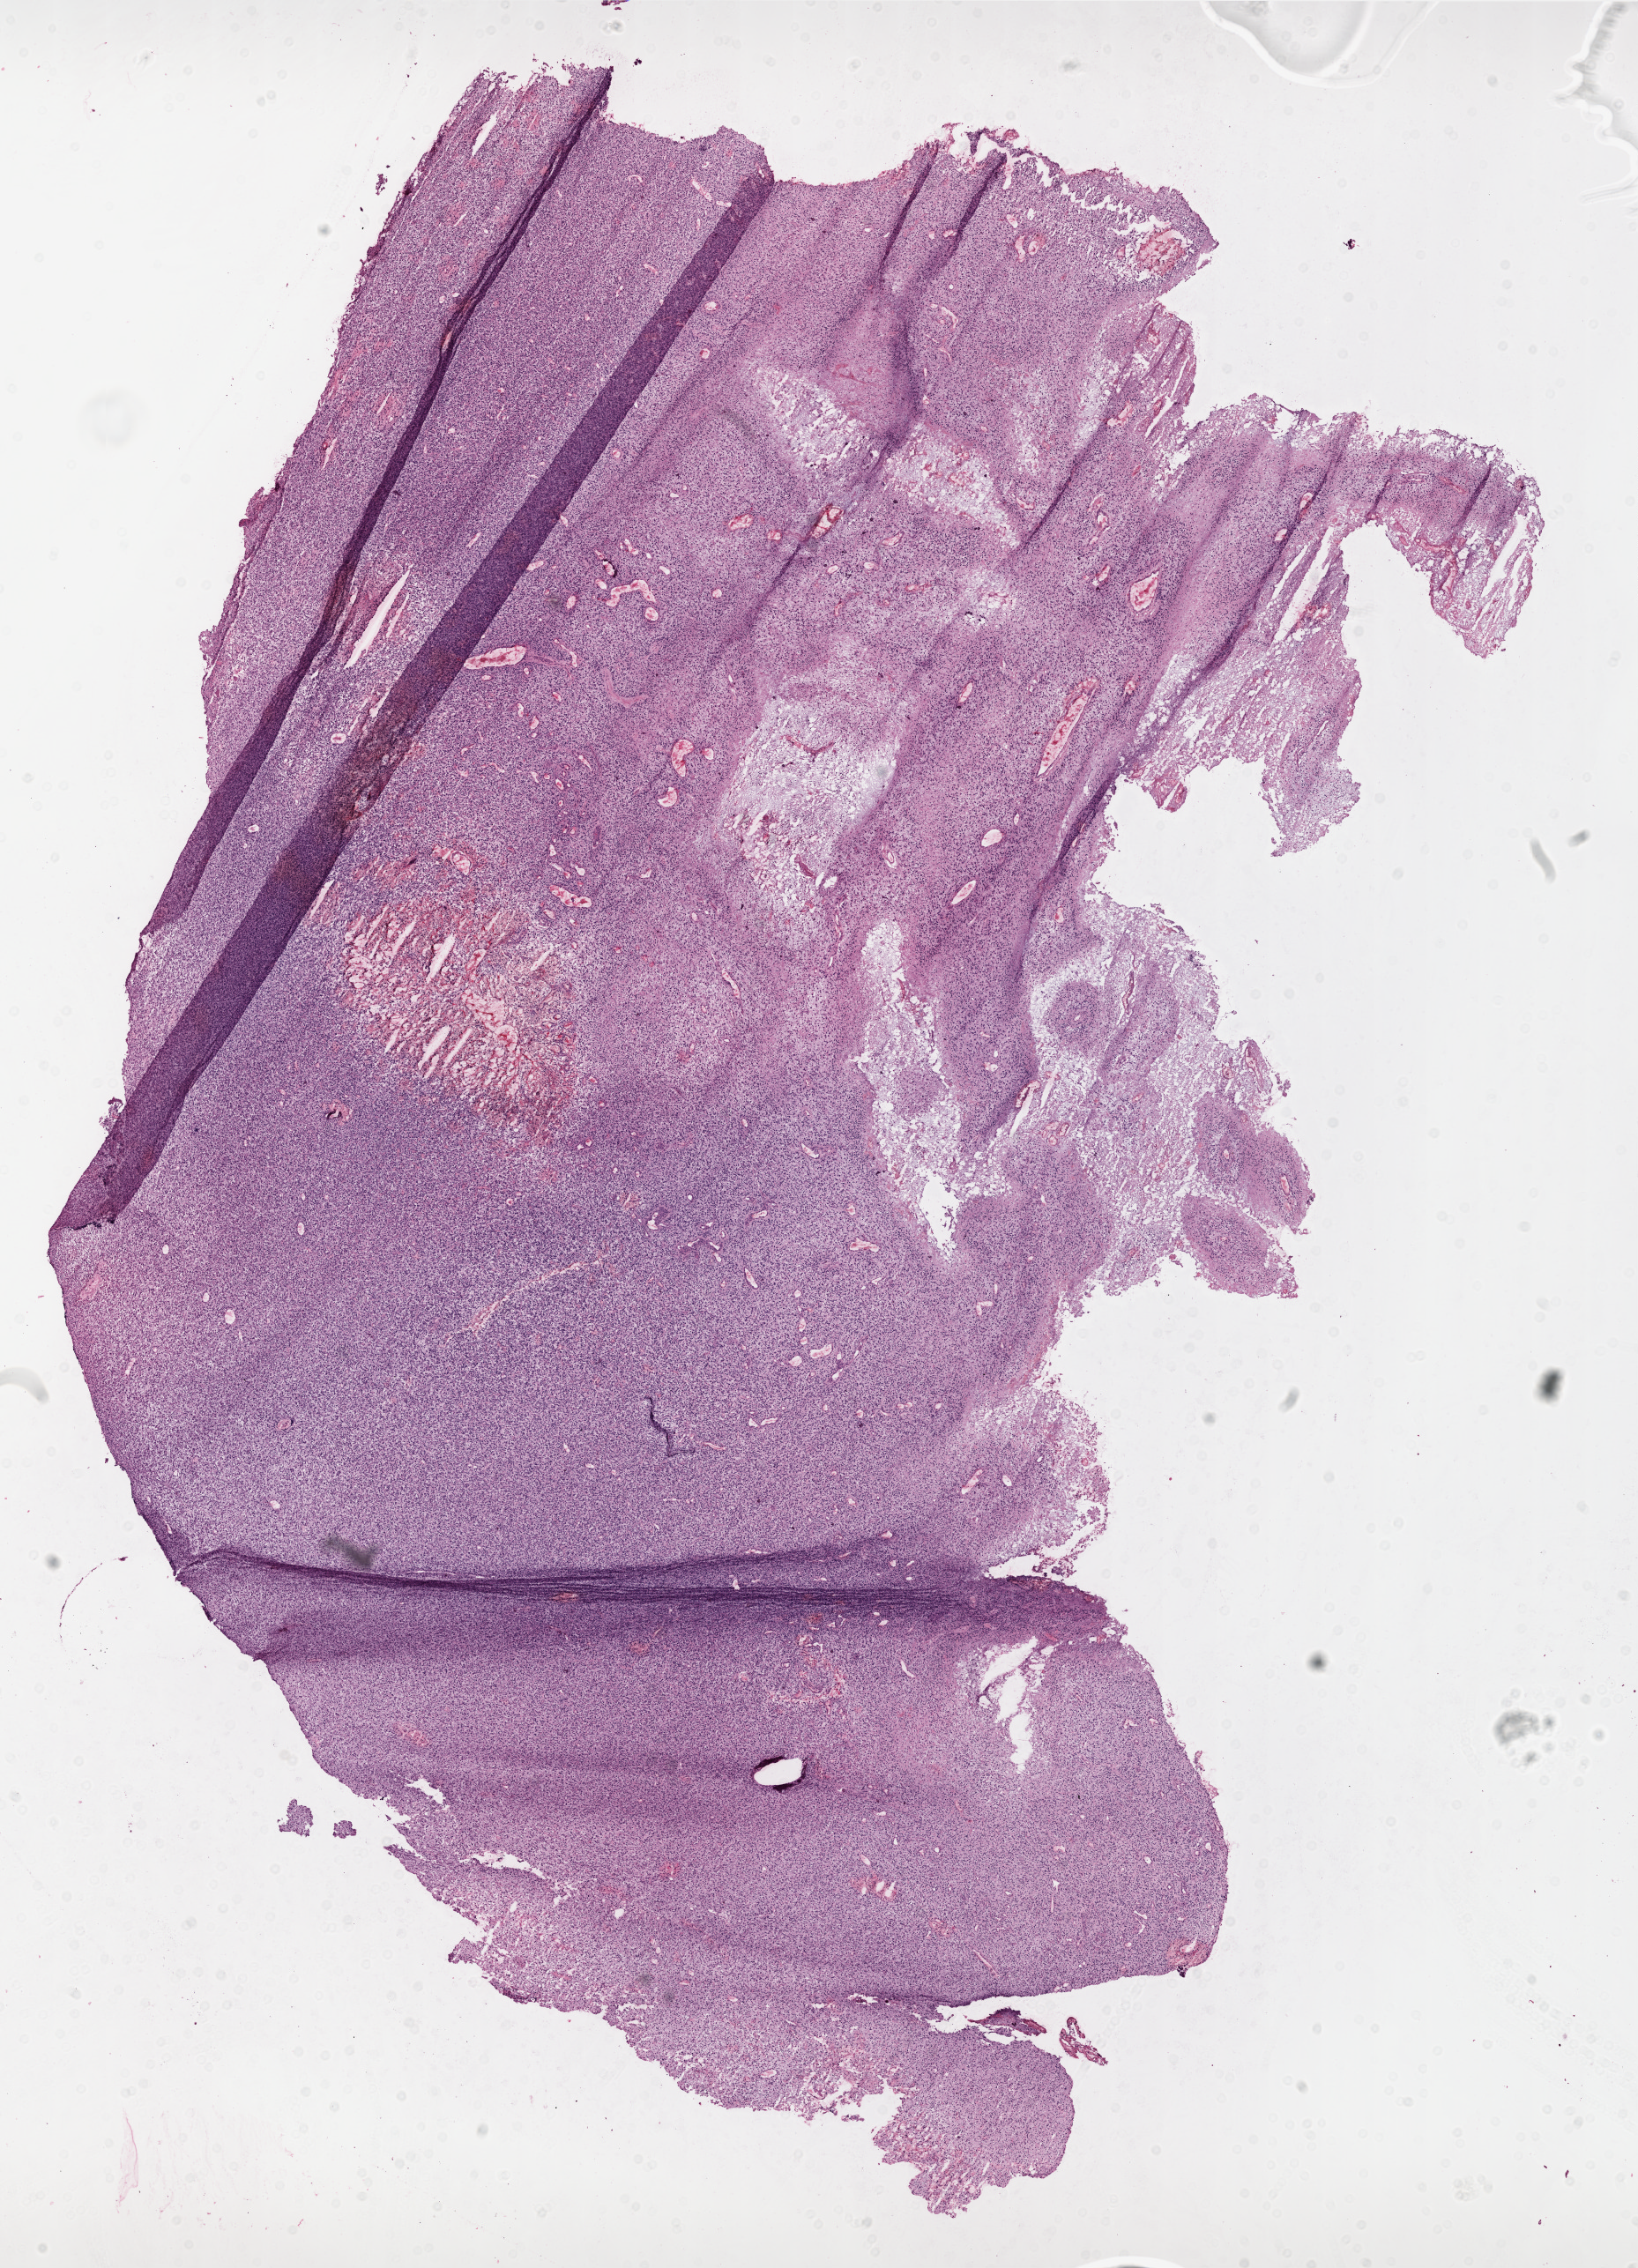
Digitized H&E-stained tissue section (whole slide), a low-resolution overview of the entire scanned area, about 14.9 x 20.7 mm; frozen section from the top of the tissue portion; sample: primary tumour, brain. Male, age 51 years at initial diagnosis. Composition of this section per pathologist review: tumour cells 80%, tumour nuclei 100%, normal cells 0%, stromal cells 0%, necrosis 20%.
Pathologic diagnosis: Glioblastoma.